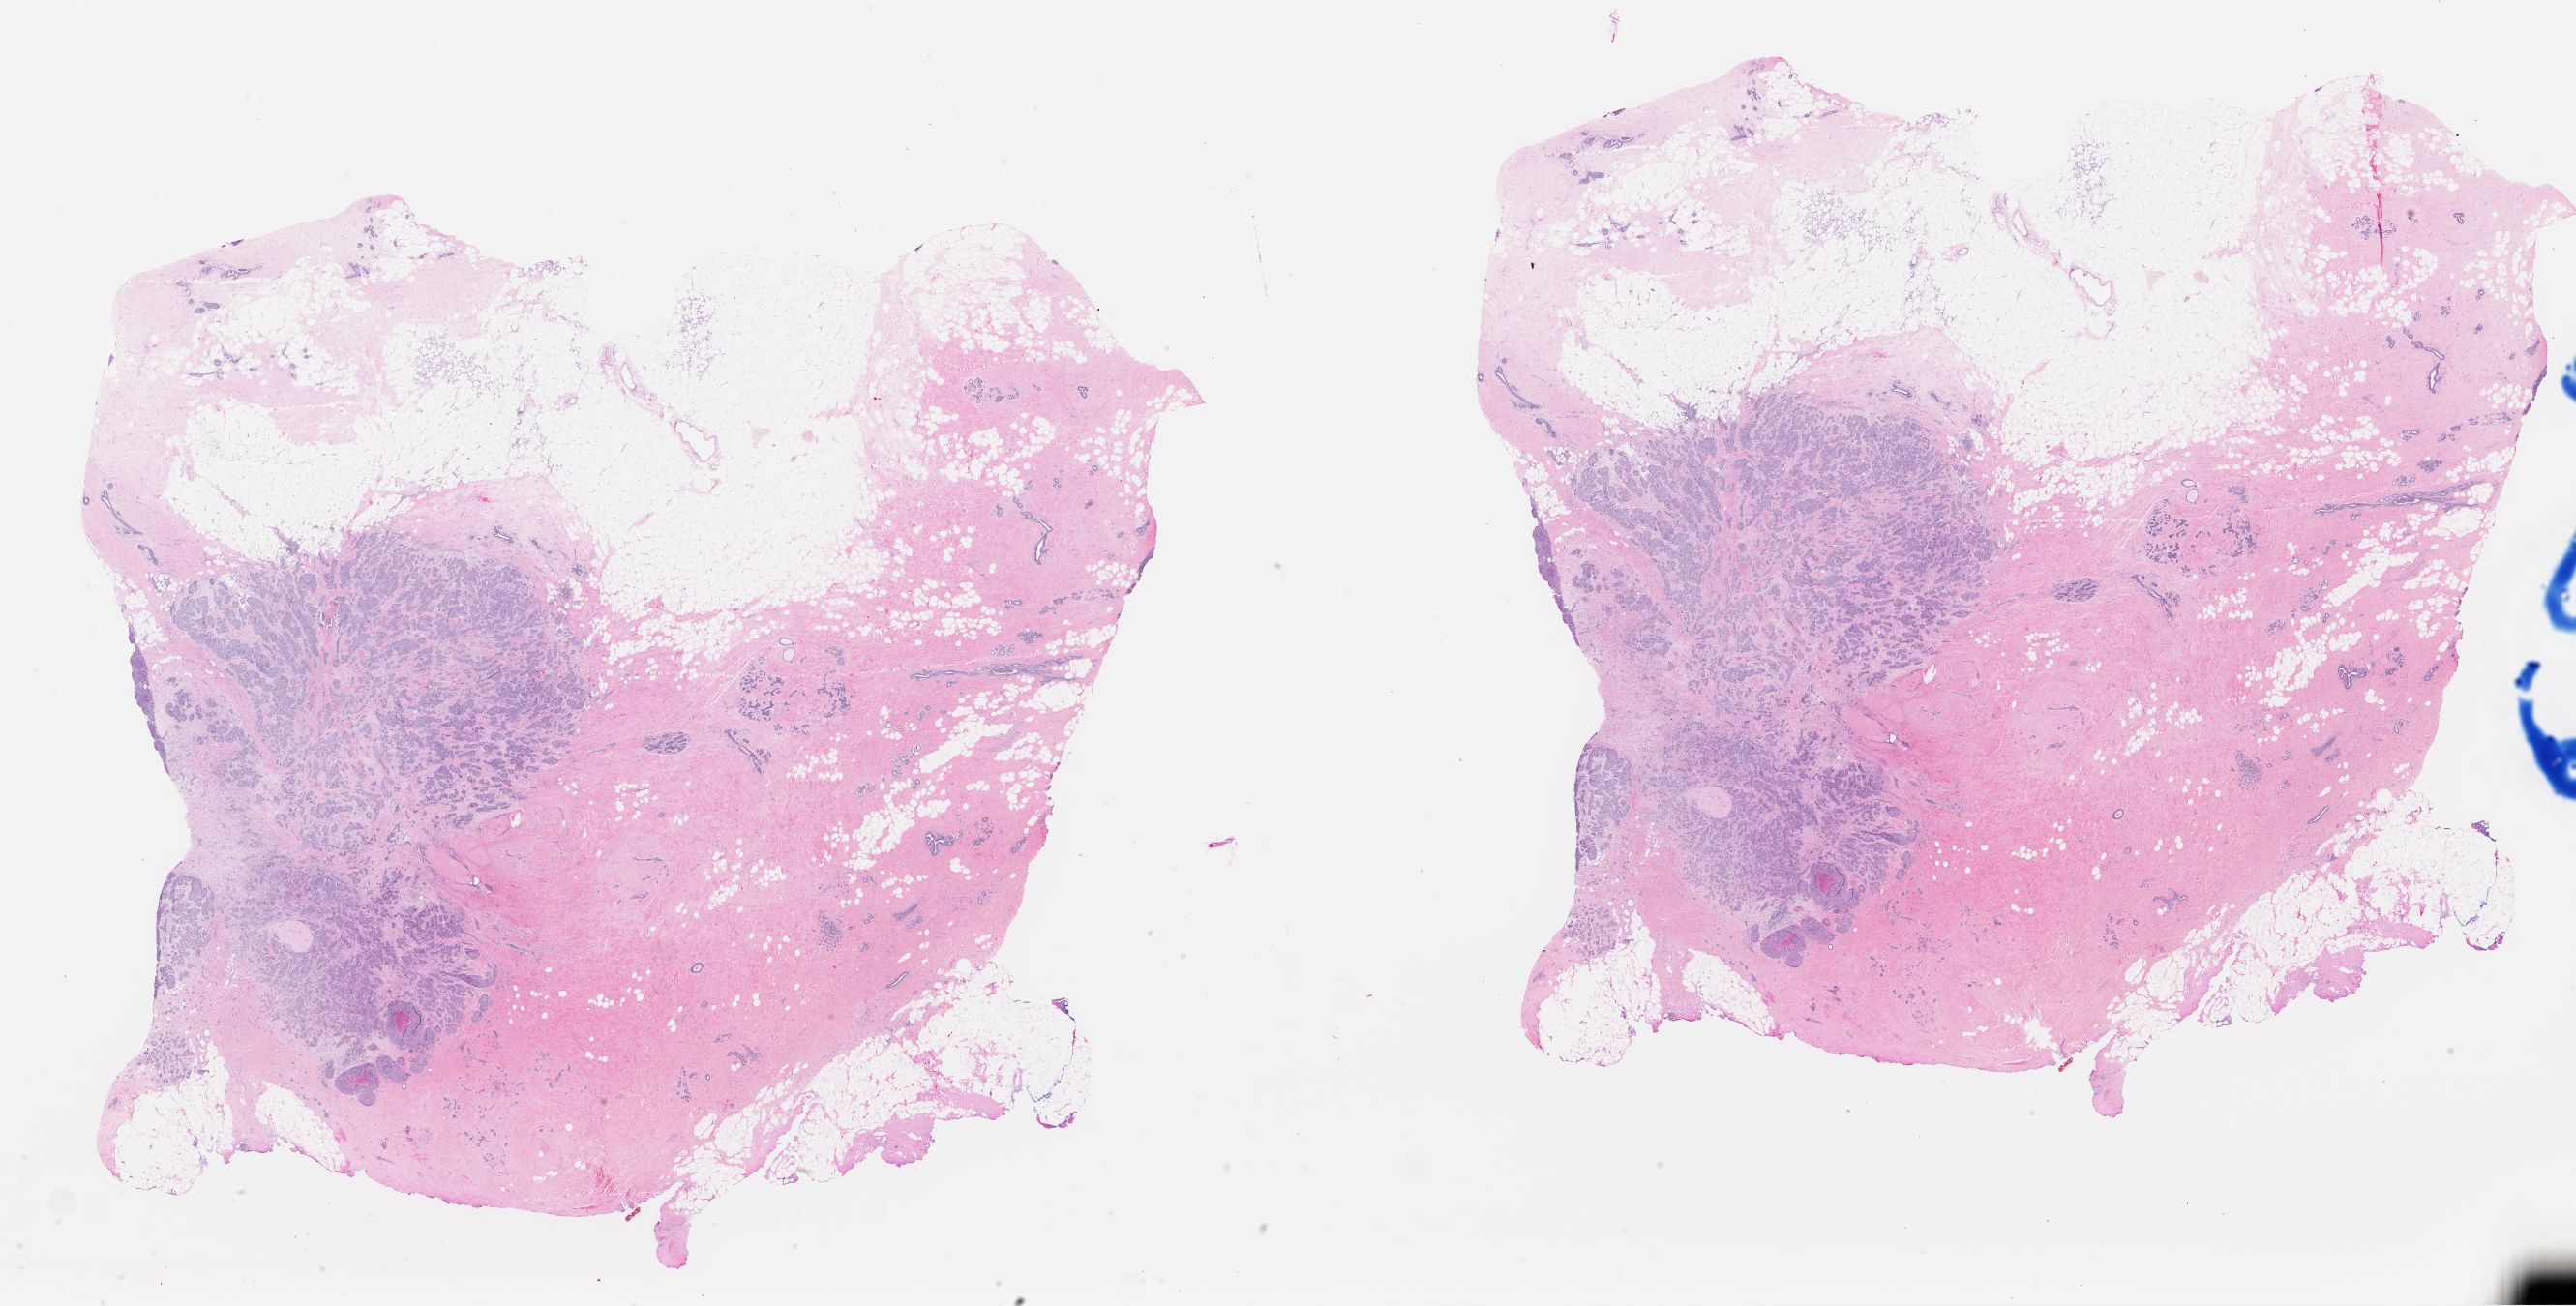
H&E whole-slide image — whole scanned area (about 42.1 x 21.3 mm, acquisition: 40x scan) shown as a low-resolution overview; FFPE section; sample: primary tumour, breast. Female patient; age at initial diagnosis 70 years.
Pathologic diagnosis: Infiltrating duct carcinoma, NOS. AJCC pathologic stage: I (6th edition). Laterality: left.